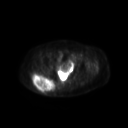
FDG PET of an extremity soft-tissue mass (from a PET/CT study), one axial slice; position 54 of 267 along the scan axis; 3.27 mm slice thickness; 128 × 128 image matrix, field of view 600 × 600 mm. Patient: female, 60 years. From the clinical record (not read from this slice): histological type: spindle cell suggestive of myxofibrosarcoma; grade: intermediate; site of the primary tumour: right buttock.
Structures marked on this image (expert contour drawn on MRI and transferred to this co-registered scan by the dataset authors):
- gross tumour volume (mass): bounding box <33,73,56,94> (left, top, right, bottom; pixels)